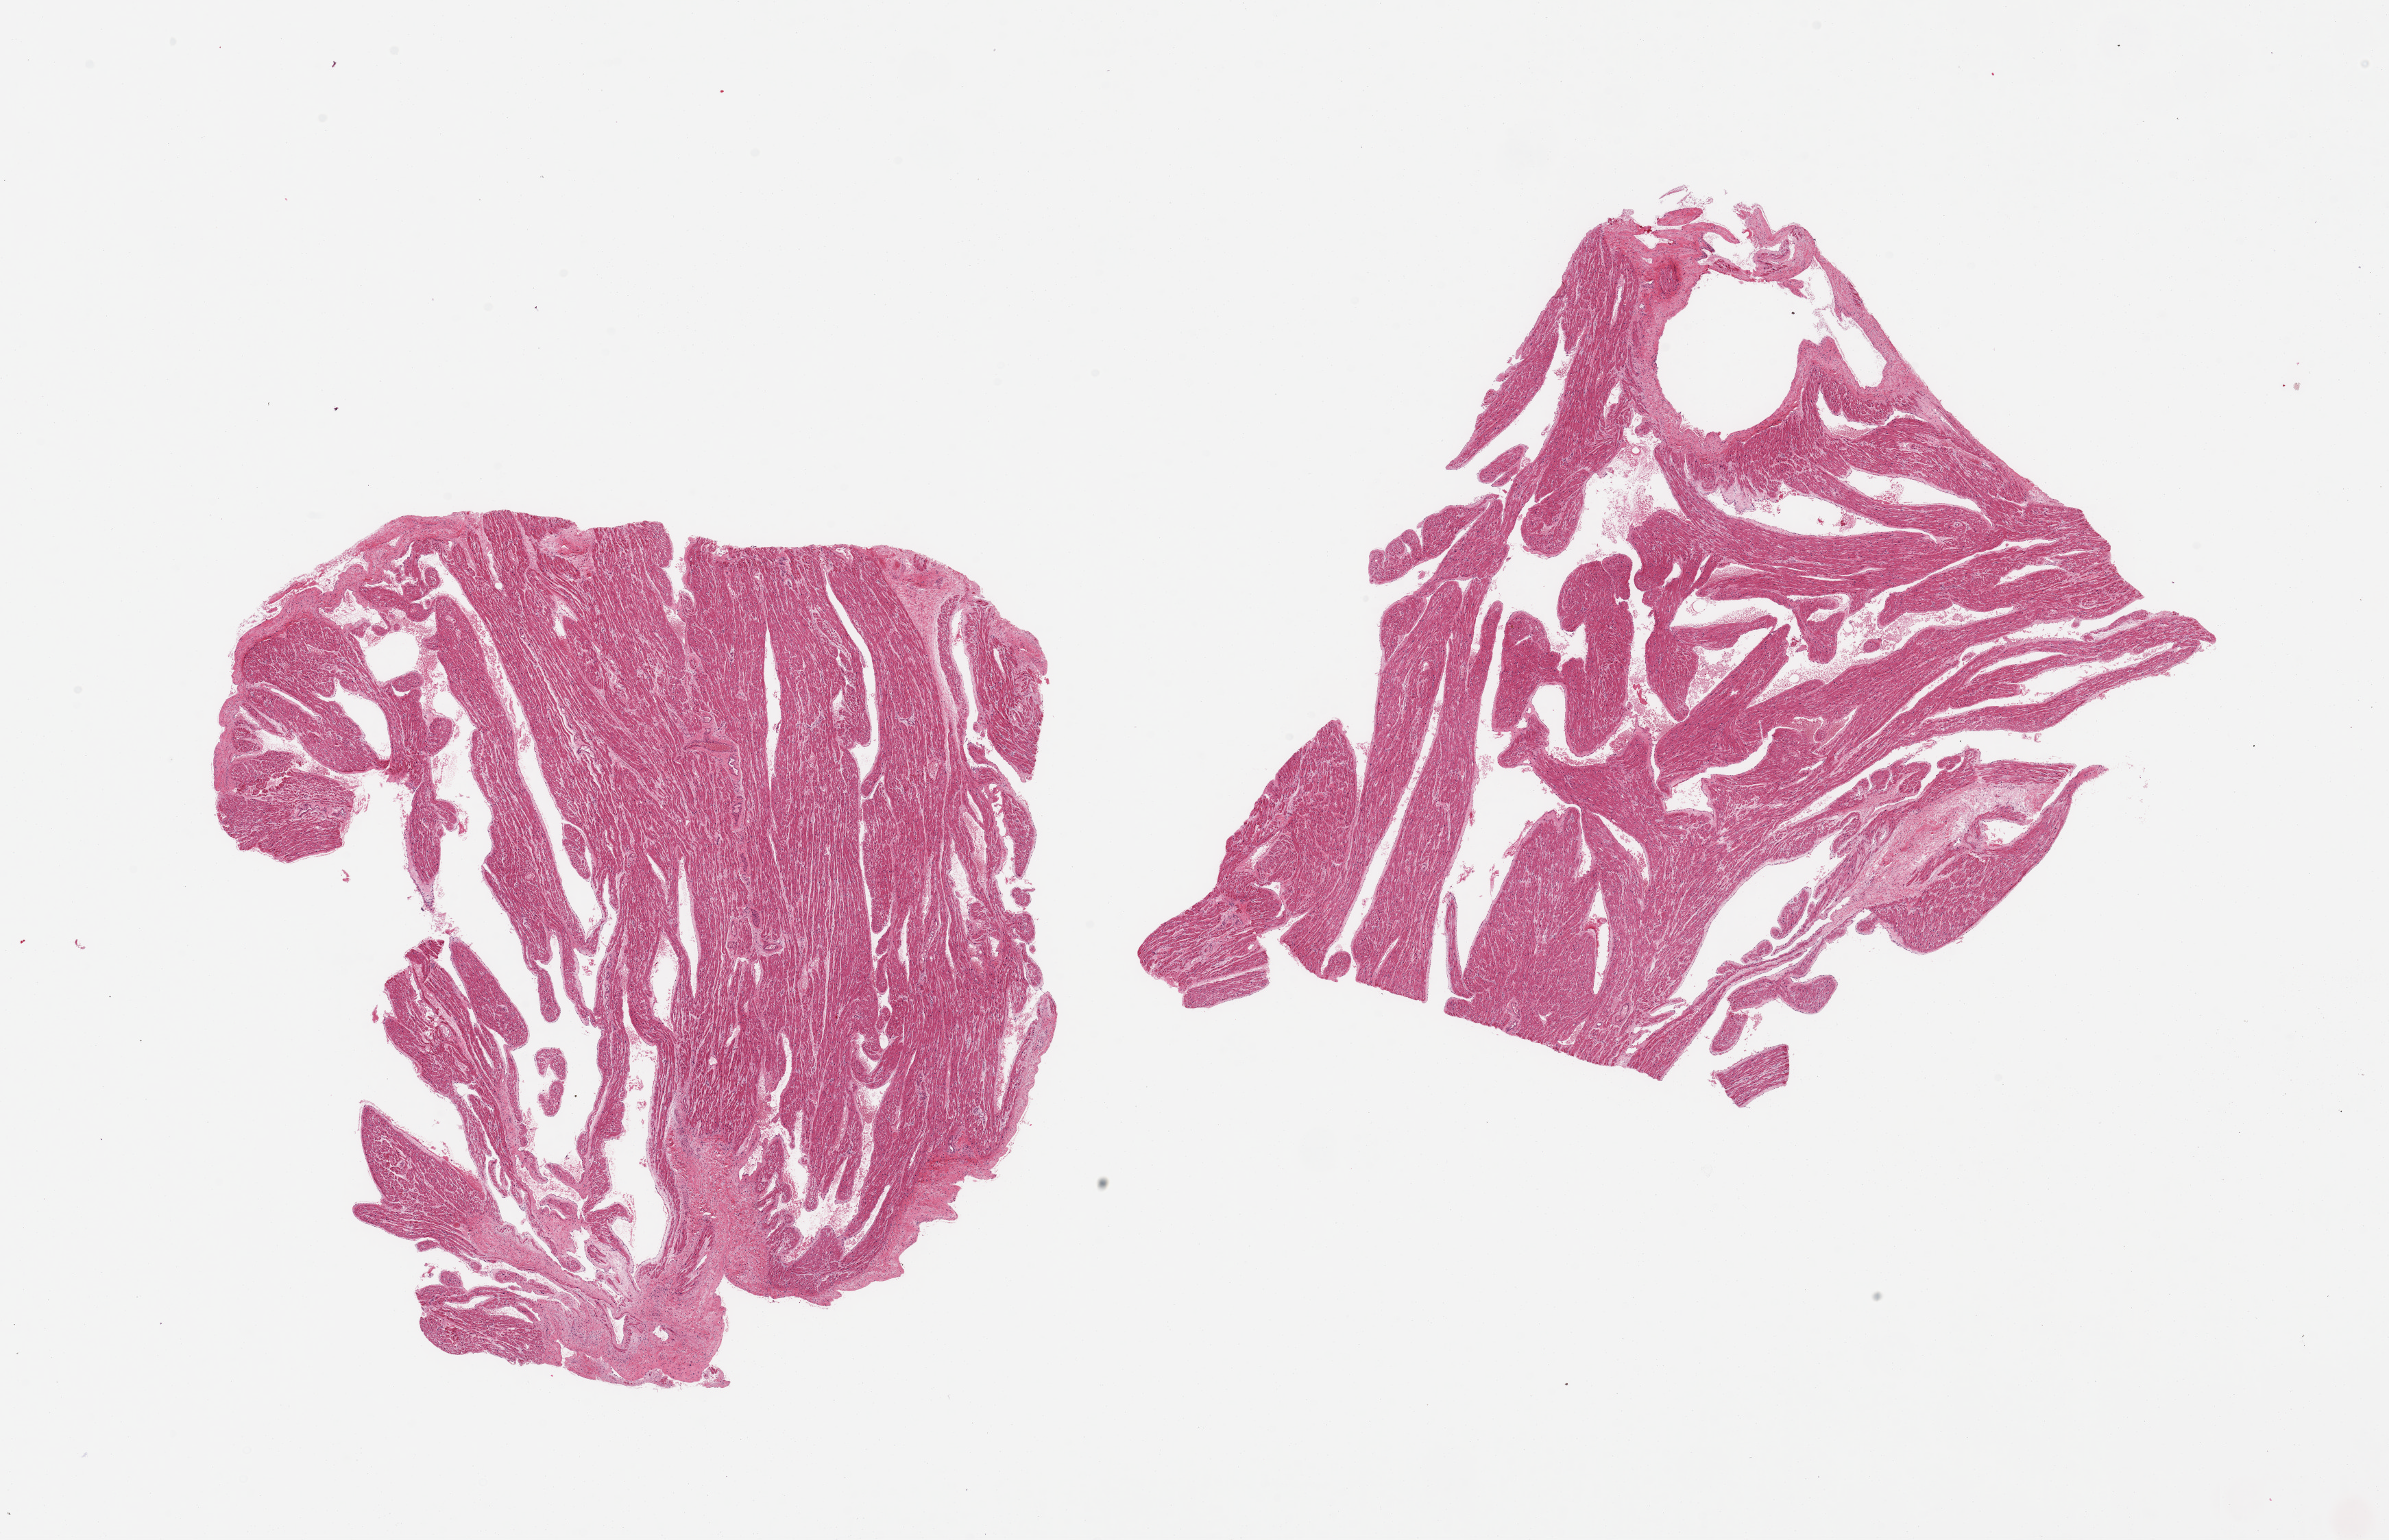
H&E whole-slide image — low-resolution overview of the scanned area, about 27.6 x 17.8 mm; PAXgene-fixed, paraffin-embedded tissue; sampled site (target tissue): auricular appendage; donor tissue sample. Donor: male.
Reviewer comment on this tissue sample: 2 pieces; minimal fibrofatty tissue.